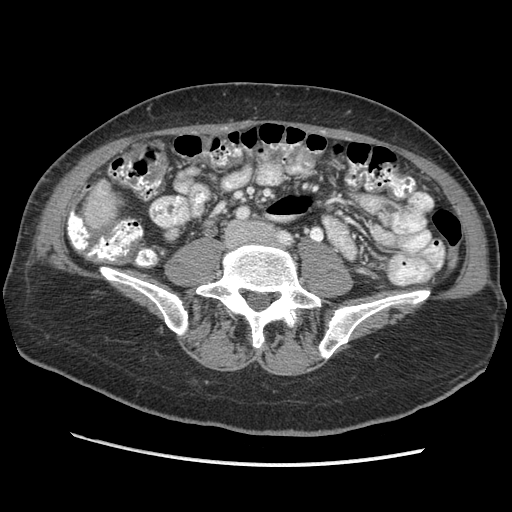
Contrast-enhanced abdominal CT (liver protocol), one axial slice. Position 78 of 170 along the scan axis. Reconstruction kernel STANDARD. 140 kVp. Soft-tissue window (W 400 / L 40 HU). 512 × 512 image matrix, field of view 360 × 360 mm. From the clinical record (not read from this slice): diagnosis: hepatocellular carcinoma (patient treated with transarterial chemoembolisation; whether this scan precedes or follows treatment is not stated here); TNM stage (as recorded): Stage-II; Child-Pugh class: A; tumour nodularity: multinodular; tumour size: 4 cm.
Annotated regions visible in this slice (semi-automatically segmented with operator editing):
- liver parenchyma outside the tumour (the mass and vessels are separate outlines, so this box may not span the whole liver): box from (x=84, y=180) to (x=116, y=228) px